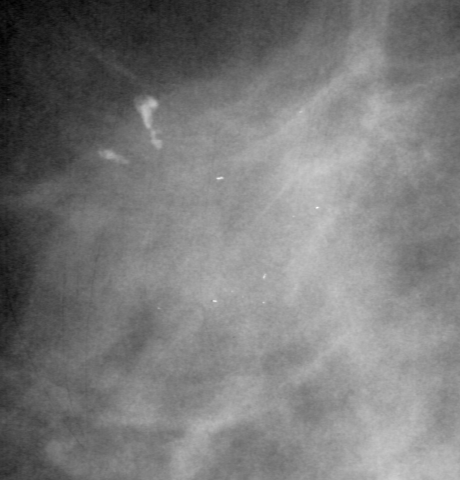
Crop from a digitized film mammogram around one marked abnormality, left breast, MLO view.
- Finding: mass, shape irregular, margins spiculated; BI-RADS assessment category 4; subtlety rating 3 on a 1 (subtle) to 5 (obvious) scale; pathology result (as recorded, not read from the image): malignant.